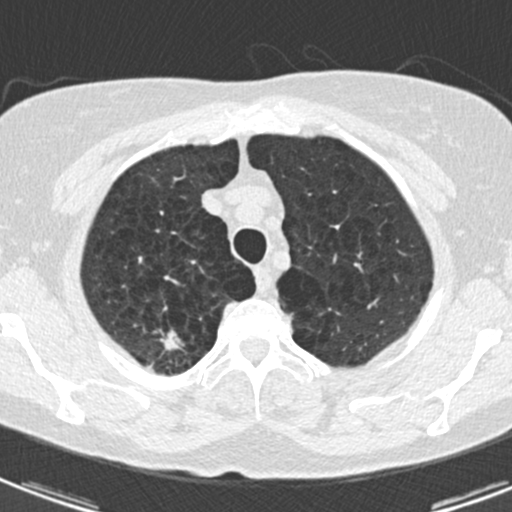
Low-dose screening chest CT, one axial slice; slice 149 of 174 in the series (ordered by position); lung window (W 1500 / L -600 HU); 512 × 512 image matrix, field of view 281 × 281 mm.
Structures marked on this image (expert manual segmentation):
- lesion 1 (tumor, upper lobe of right lung): bounding box <159,330,182,351> (left, top, right, bottom; pixels)